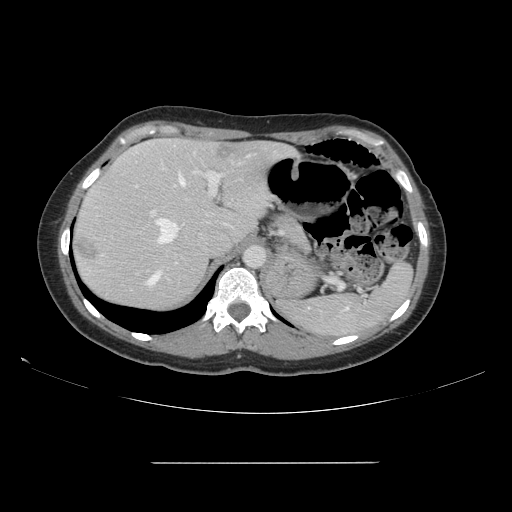
Contrast-enhanced abdominal CT, one axial slice; intravenous contrast given; soft-tissue window (W 400 / L 40 HU); 512 × 512 image matrix. Female patient, age 46 years. From the clinical record (not read from this slice): diagnosis: colorectal cancer liver metastases, imaged before liver resection; multiple liver metastases: yes; largest metastasis: 3 cm.
Annotated regions visible in this slice (manually delineated by an expert):
- hepatic veins: bounding box <155,155,251,244> (left, top, right, bottom; pixels)
- liver: <73,139,291,310>
- planned liver remnant (the part of the liver to remain after resection): <88,139,289,252>
- portal vein (with intrahepatic branches): <135,171,221,286>
- liver metastasis: <76,236,99,262>
- liver metastasis: <217,145,235,161>